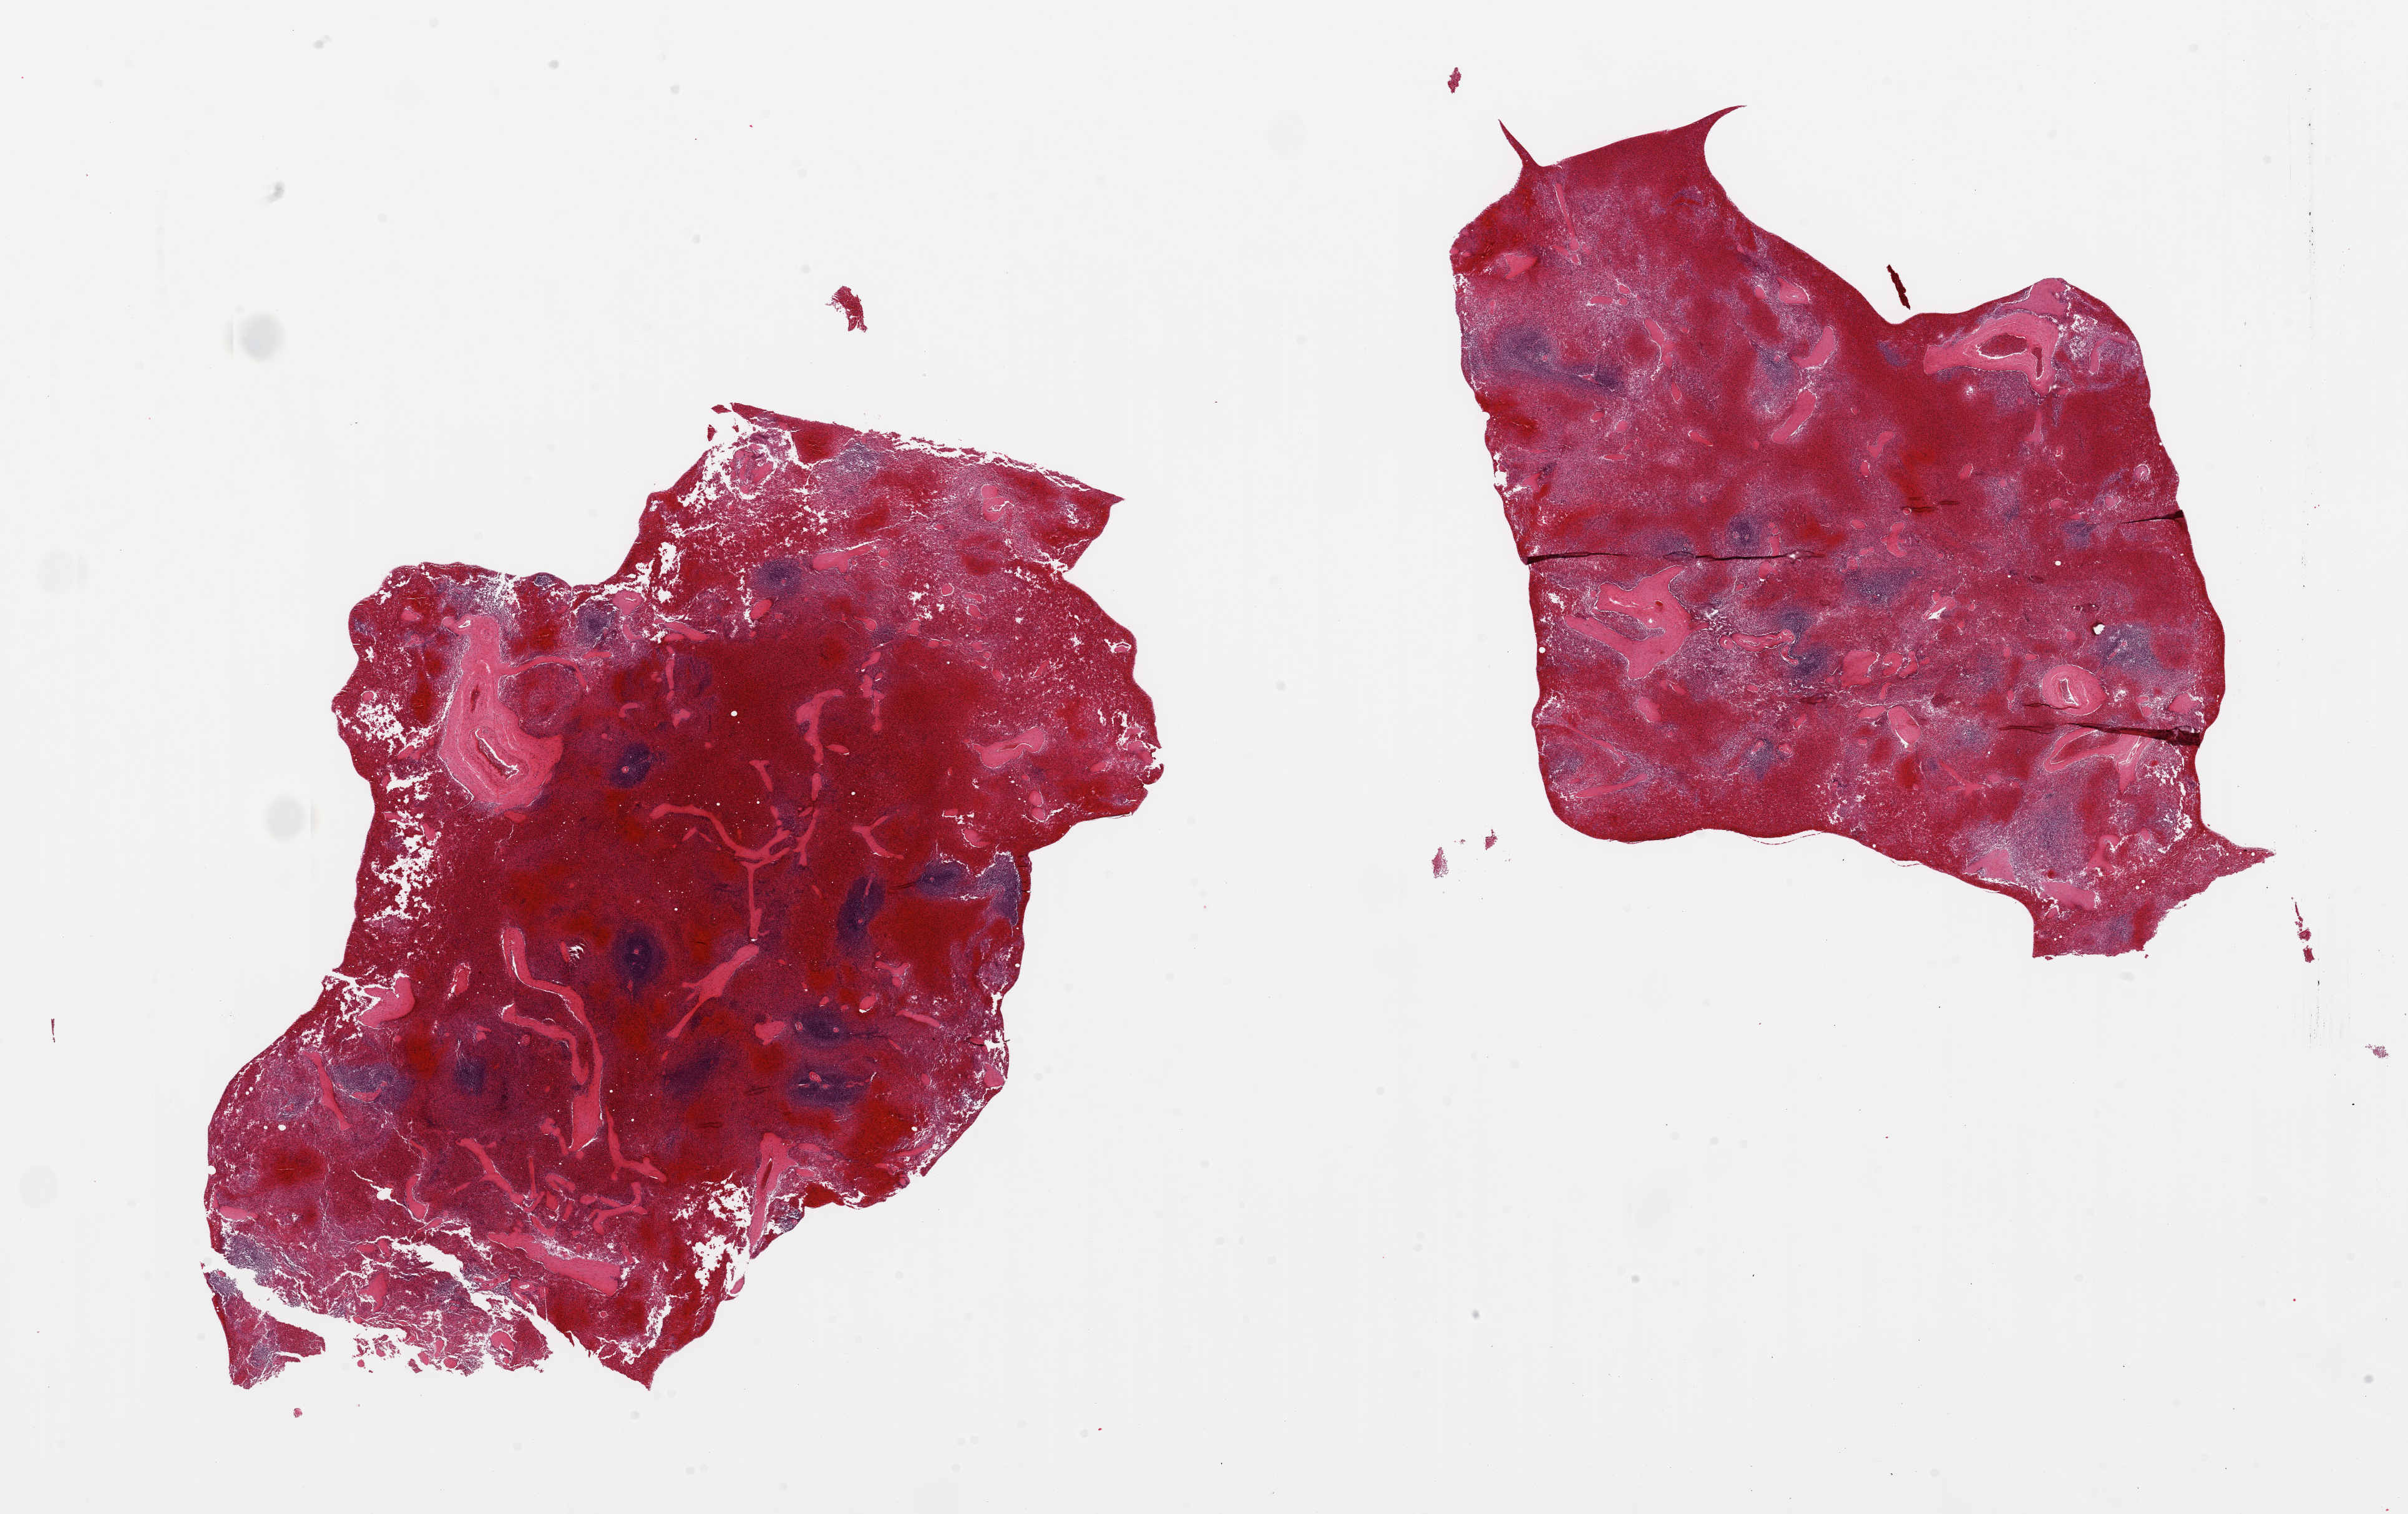
Whole-slide image, H&E stain, brightfield — a low-resolution overview of the entire scanned area, about 30.5 x 19.2 mm (from a 20x scan); PAXgene-fixed, paraffin-embedded tissue; sampled site (target tissue): spleen; tissue donor sample. Donor sex: male.
Reviewer comment on this tissue sample: 2 pieces; congested.